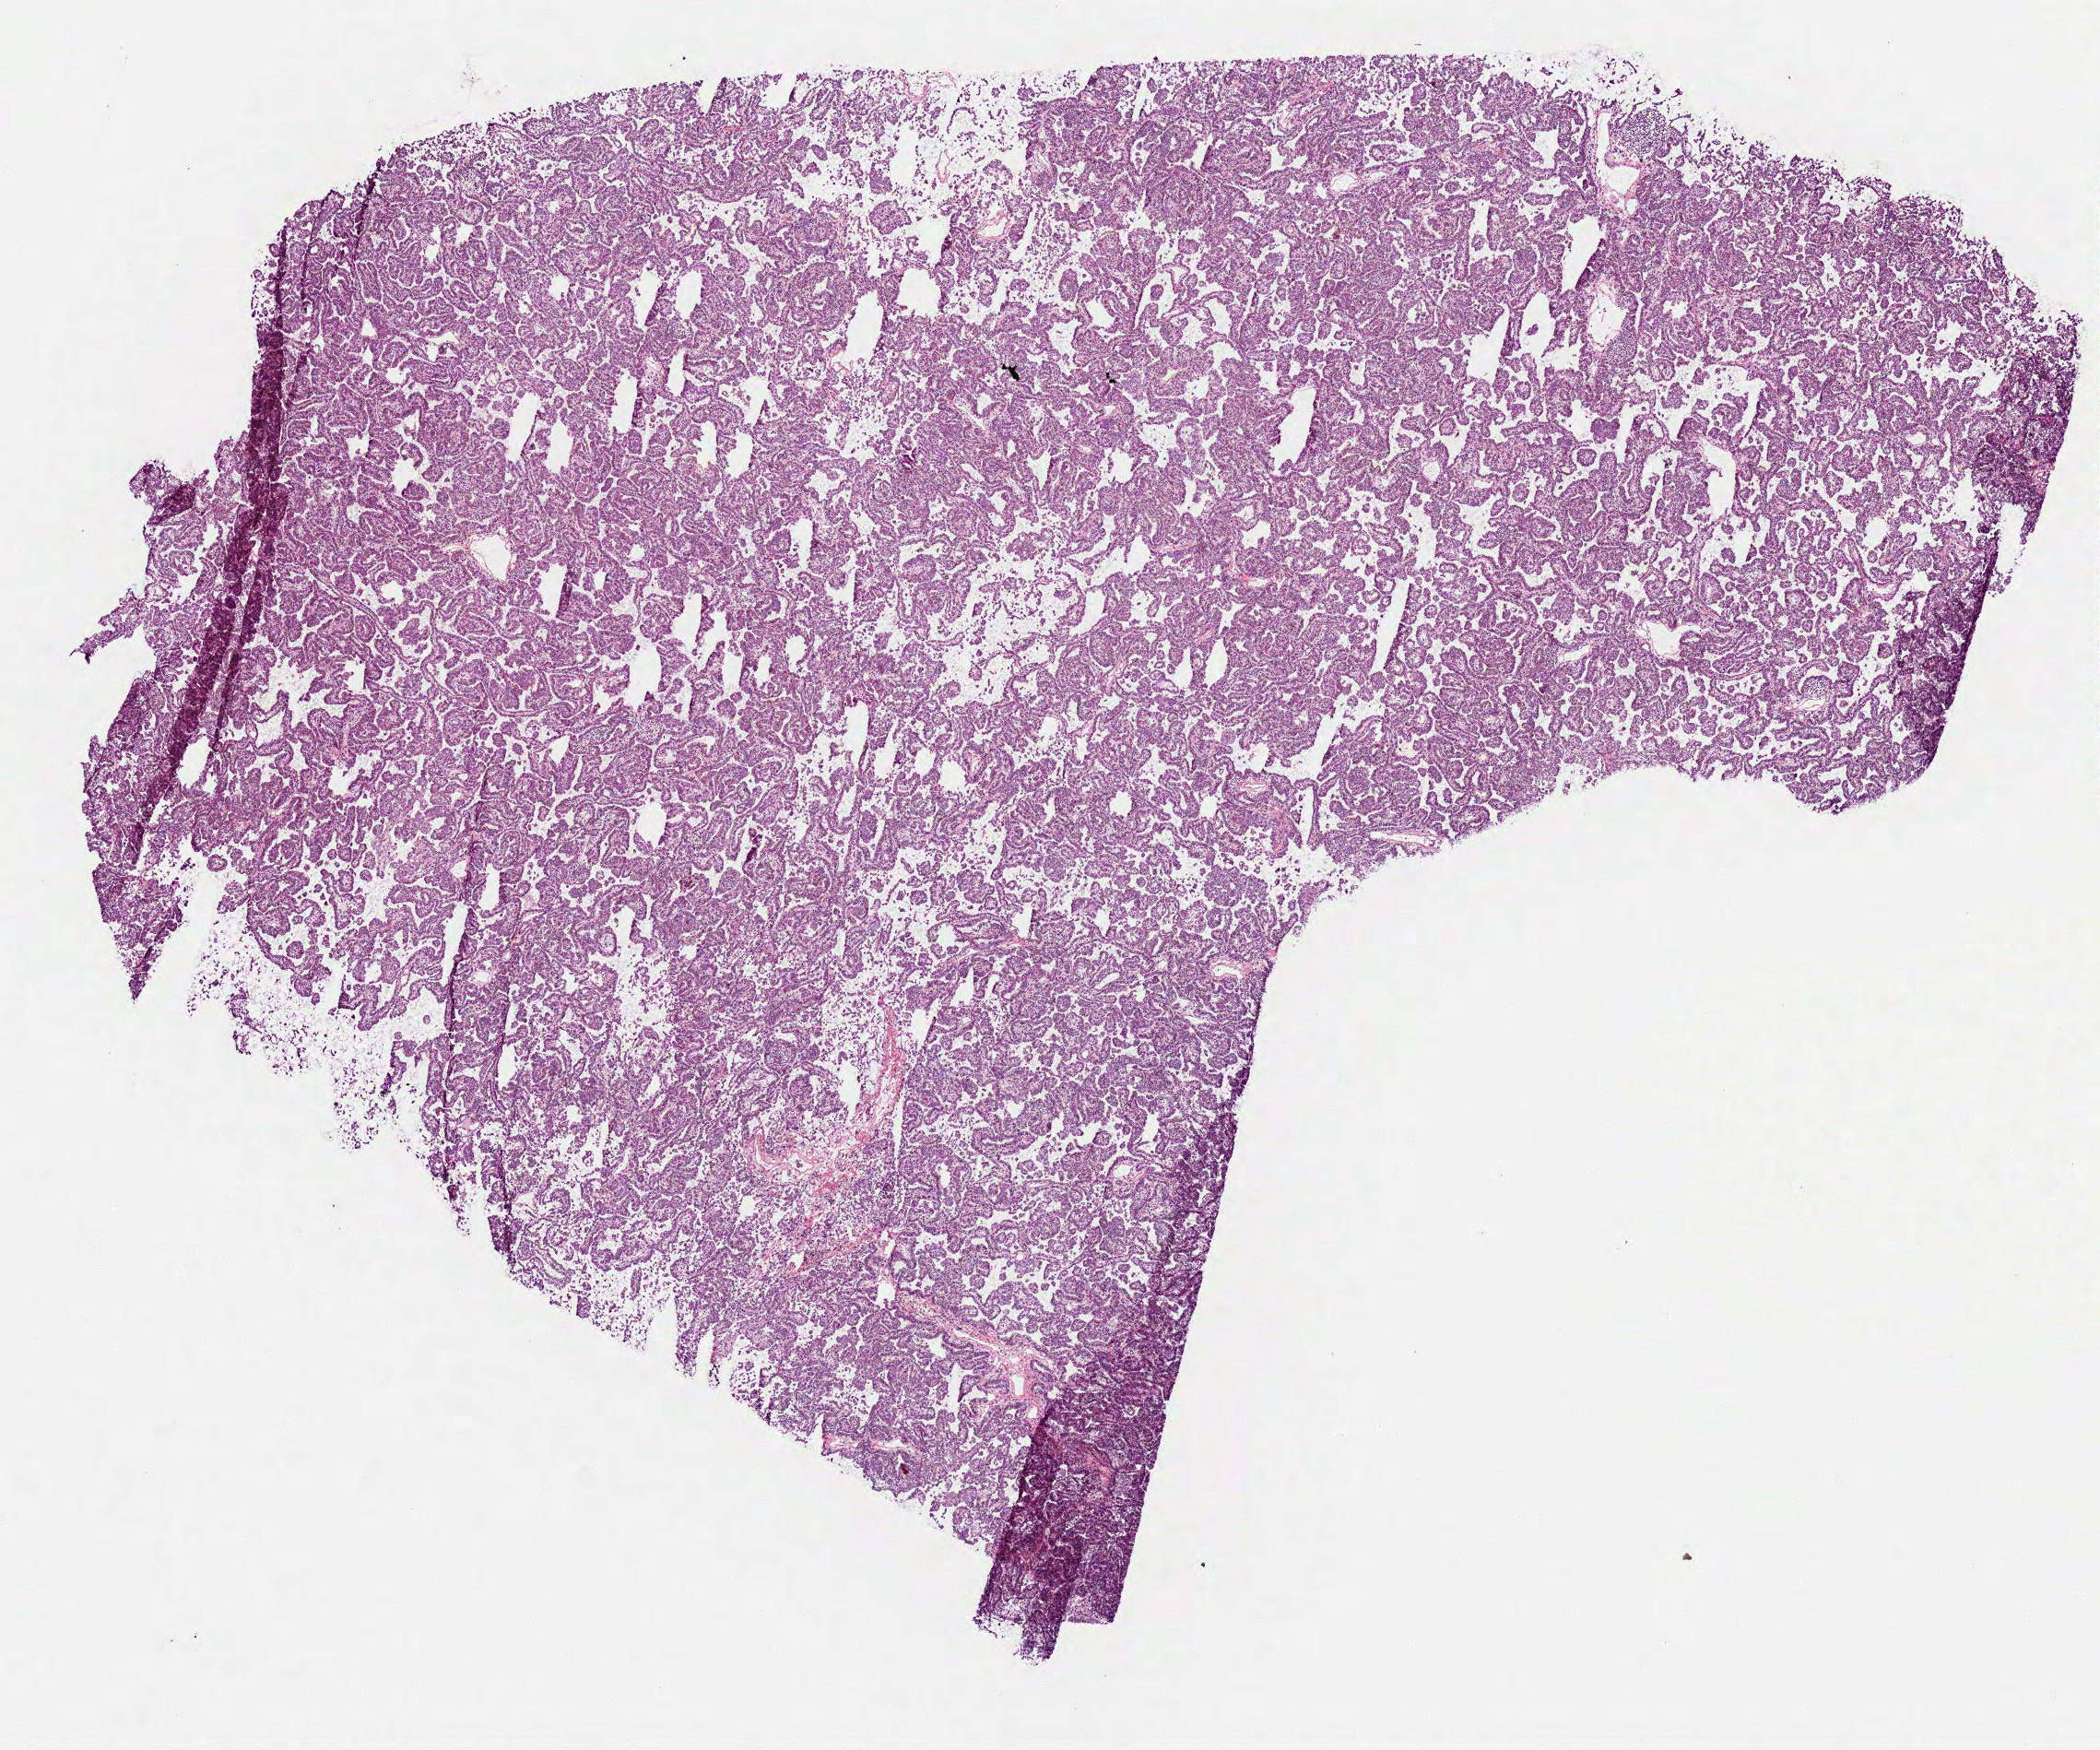
H&E whole-slide image, shown as a low-resolution overview of the whole scanned area (about 9.2 x 7.7 mm, slide scanned at 40x). Frozen section from the bottom of the tissue portion. Sample: primary tumour, lung. Male patient; age at initial diagnosis 62 years. Composition of this section per pathologist review: tumour cells 90%, tumour nuclei 80%, normal cells 0%, stromal cells 10%, necrosis 0%.
* AJCC pathologic stage: IV
* diagnosis: Adenocarcinoma with mixed subtypes